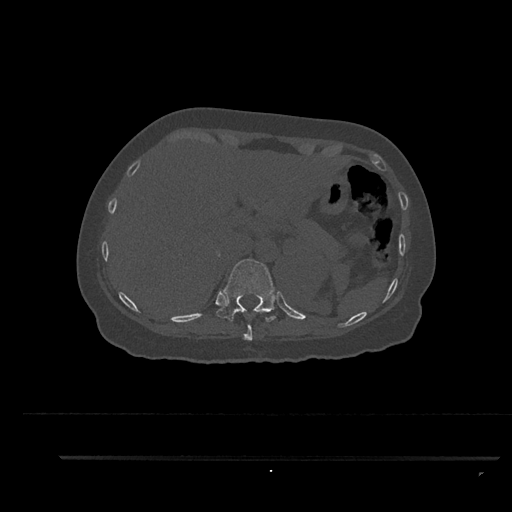
CT including the spine, one axial slice; position 329 of 797 along the scan axis; reconstruction kernel Br40s/3; 120 kVp; bone window (W 1800 / L 400 HU); 0.5 mm slice thickness; 512 × 512 image matrix, field of view 408 × 408 mm. Patient: female, 44 years. Case-level facts recorded for this patient, not image findings: primary cancer: renal; vertebrae with lytic lesions (as recorded): L1.
Structures marked on this image (semi-automatically segmented with operator editing):
- T10 vertebra: bounding box [x1, y1, x2, y2] px = [243, 309, 253, 341]
- T11 vertebra: [216, 259, 276, 322]